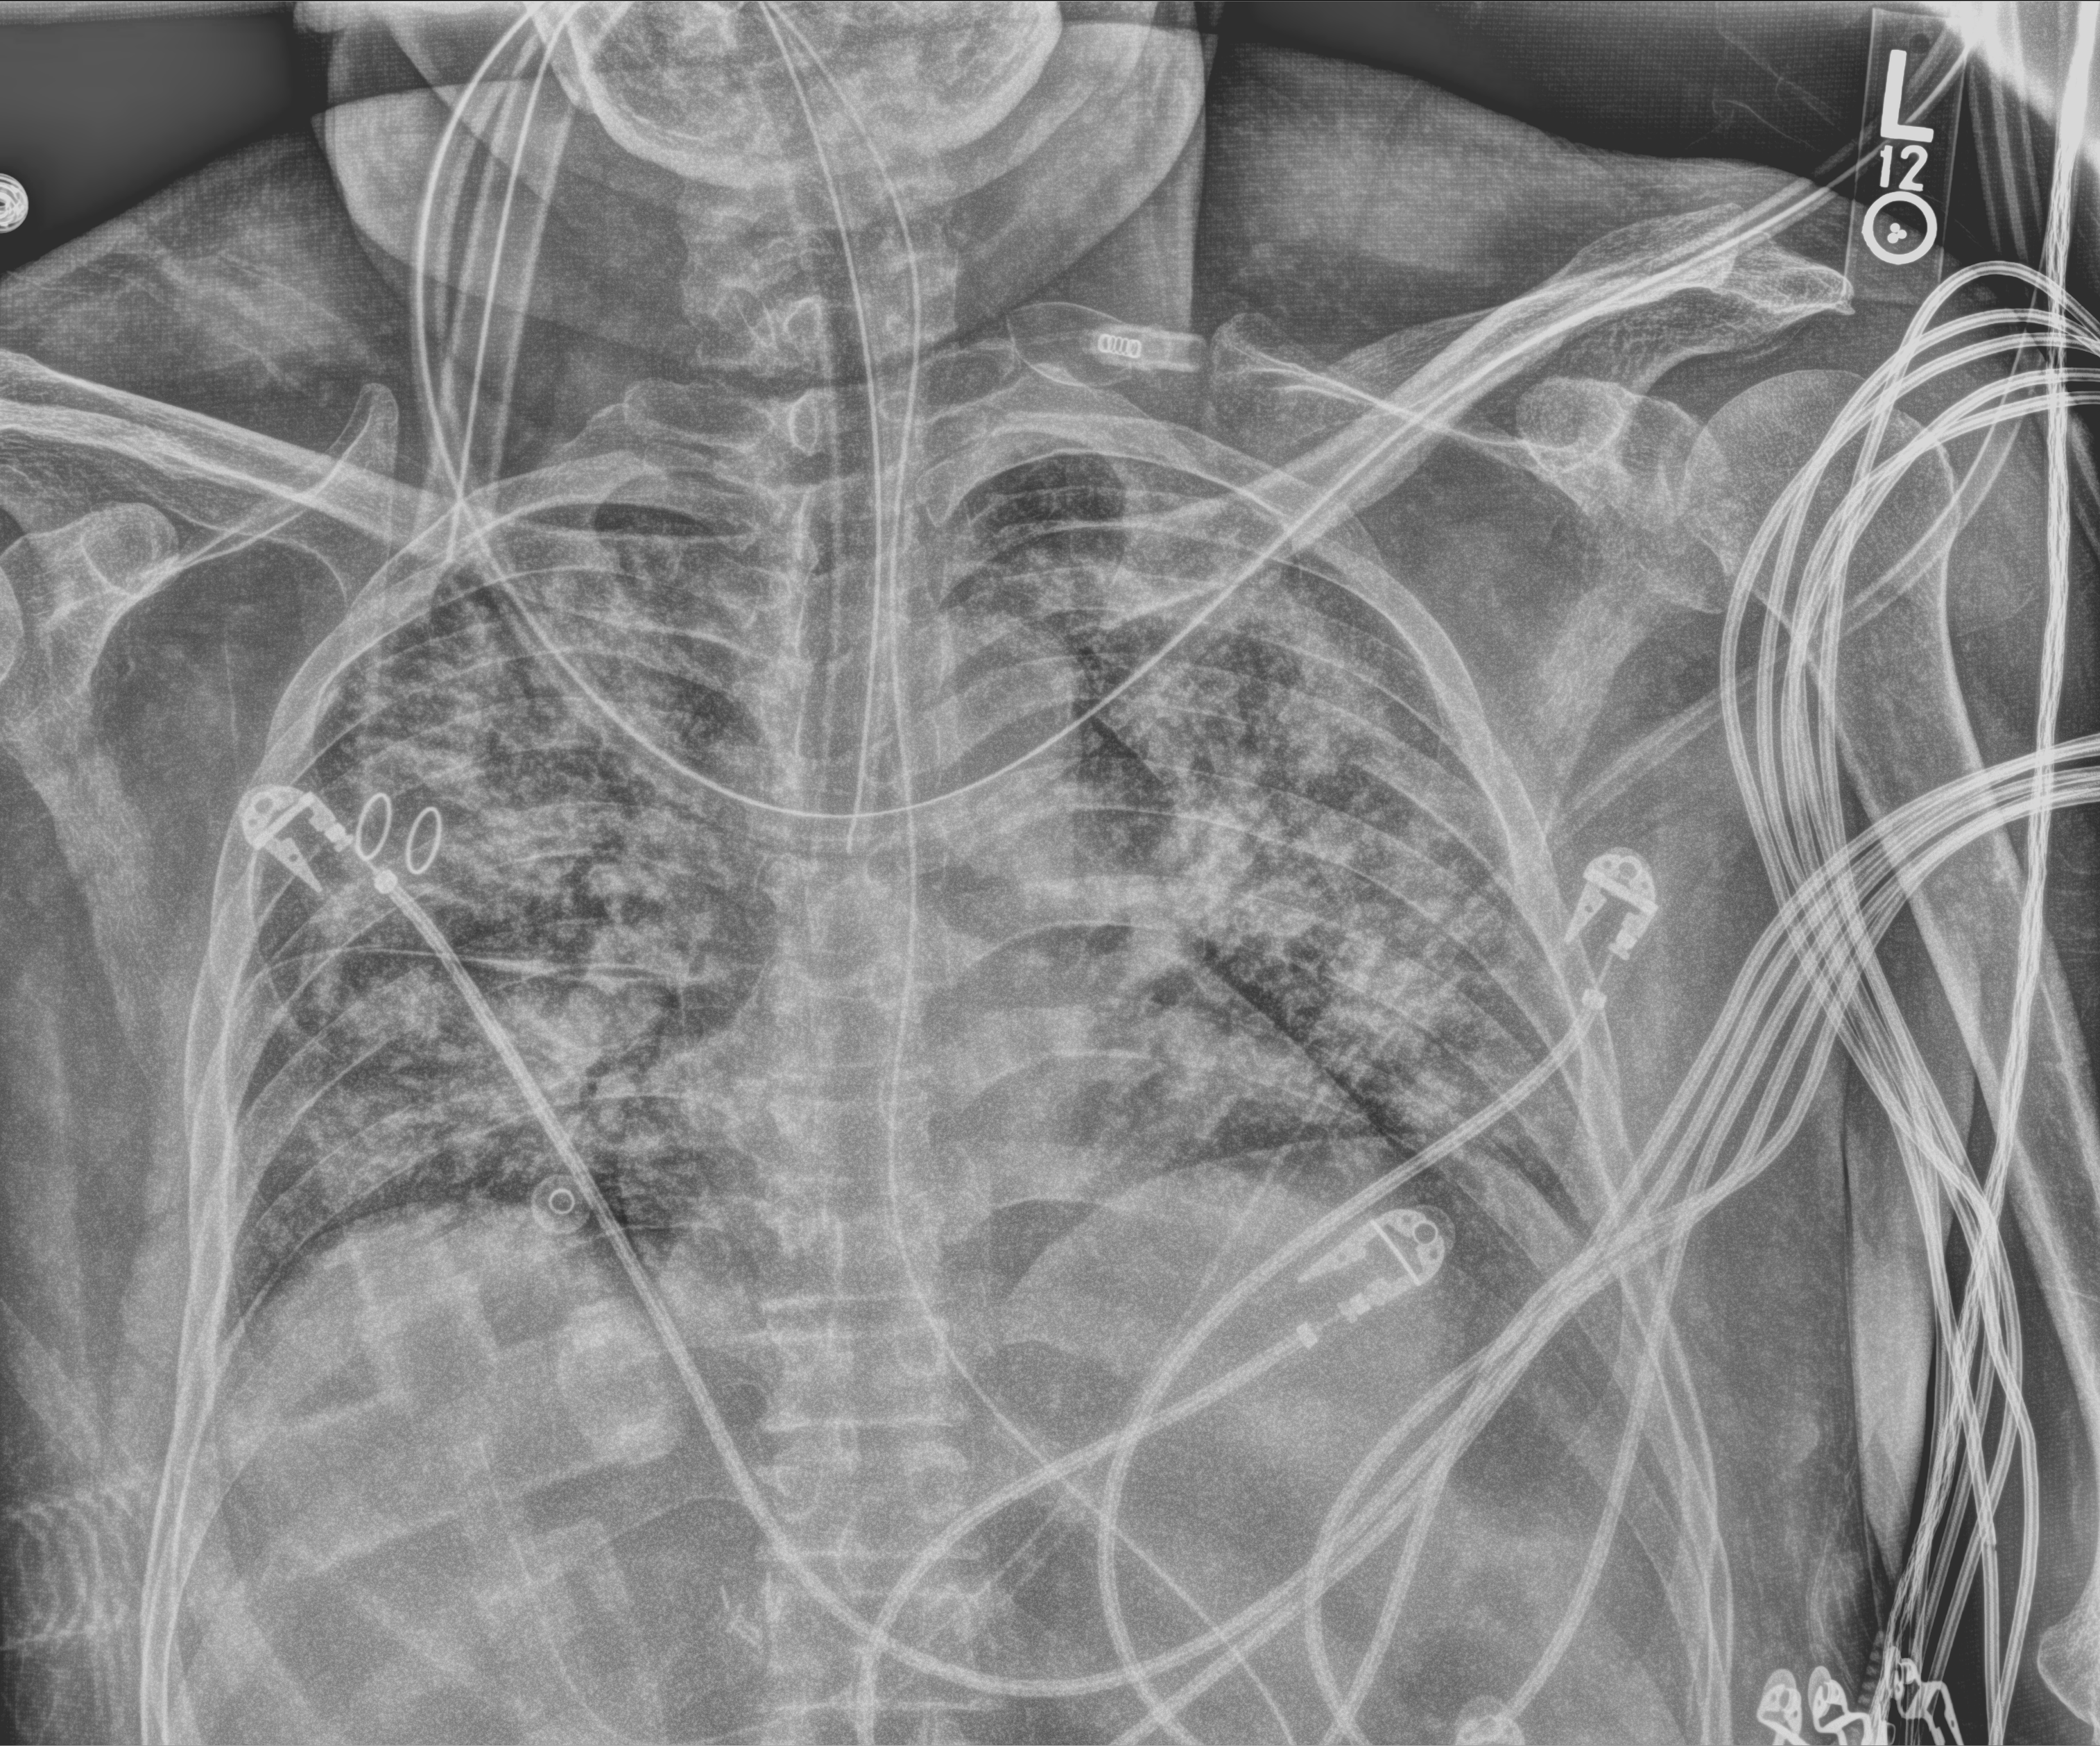
Chest X-ray (portable), anteroposterior (AP) projection. Patient hospitalised with COVID-19; male, aged 60–74 years.
From the hospital-stay record, not from the radiograph (when in the stay this image was taken is not recorded):
- admitted to intensive care during this hospital stay: yes
- length of hospital stay: 23 days